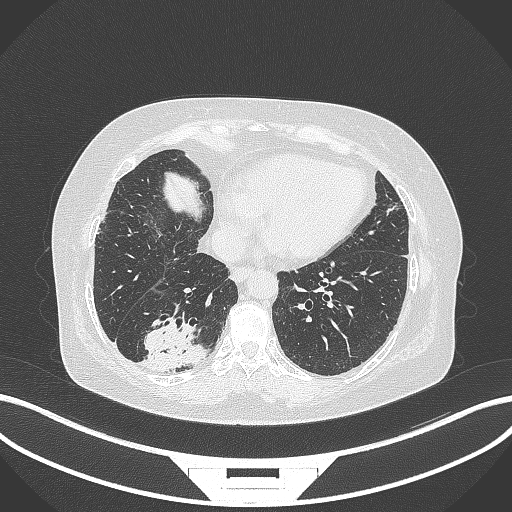
Chest CT, one axial slice; slice 69 of 296 in the series (ordered by position); reconstruction kernel B70f; lung window (W 1500 / L -600 HU); 1 mm slice thickness; 512 × 512 image matrix, field of view 400 × 400 mm. Female patient, age 65 years. From the clinical record (not read from this slice): clinical TNM (as recorded): T2b N1 M0; histopathological grade: G1.
Outlined on this slice (rectangle marked by the reading radiologist):
- lung tumour (recorded histology: adenocarcinoma): bounding box [x1, y1, x2, y2] px = [138, 319, 208, 373]